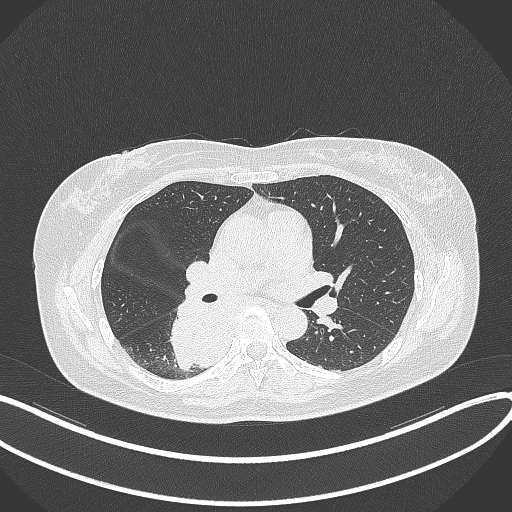
Chest CT, one axial slice. Reconstruction kernel B70f. Lung window (W 1500 / L -600 HU). 1 mm slice thickness. 512 × 512 image matrix, field of view 400 × 400 mm. Female patient, age 54 years. From the clinical record (not read from this slice): clinical TNM (as recorded): T4 N0 M0.
Structures marked on this image (rectangle marked by the reading radiologist):
- lung tumour (recorded histology: adenocarcinoma): bounding box [x1, y1, x2, y2] px = [165, 299, 235, 375]